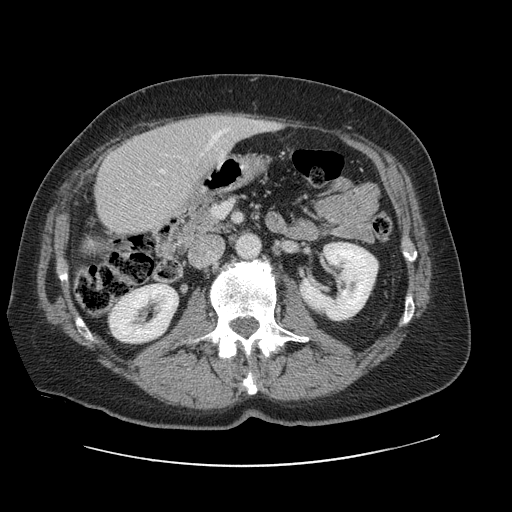
Contrast-enhanced abdominal CT, one axial slice; slice 33 of 138 in the series (ordered by position); 120 kVp; intravenous contrast given; soft-tissue window (W 400 / L 40 HU); 2.5 mm slice thickness; 512 × 512 image matrix, field of view 402 × 402 mm. Male patient, age 71 years. From the clinical record (not read from this slice): diagnosis: colorectal cancer liver metastases, imaged before liver resection; multiple liver metastases: no; largest metastasis: 3.3 cm; disease in both lobes: no.
Outlined on this slice (expert manual segmentation):
- hepatic veins: bounding box (x1, y1, x2, y2) in pixels: (201, 130, 225, 155)
- liver: (96, 115, 271, 236)
- planned liver remnant (the part of the liver to remain after resection): (96, 133, 187, 236)
- portal vein (with intrahepatic branches): (160, 169, 165, 173)